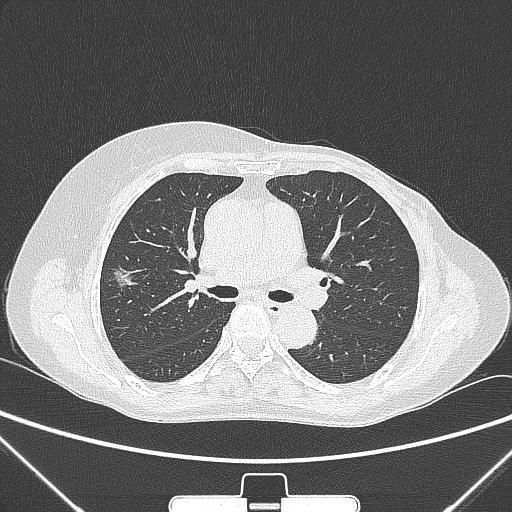
Chest CT, one axial slice; 120 kVp; lung window (W 1500 / L -600 HU); 1 mm slice thickness; 512 × 512 image matrix, field of view 350 × 350 mm. Female patient, age 64 years. Case-level facts recorded for this patient, not image findings: clinical TNM (as recorded): T1c N0 M0; histopathological grade: G1-2.
Outlined on this slice (rectangle marked by the reading radiologist):
- lung tumour (recorded histology: adenocarcinoma): bounding box [x1, y1, x2, y2] px = [107, 259, 139, 303]